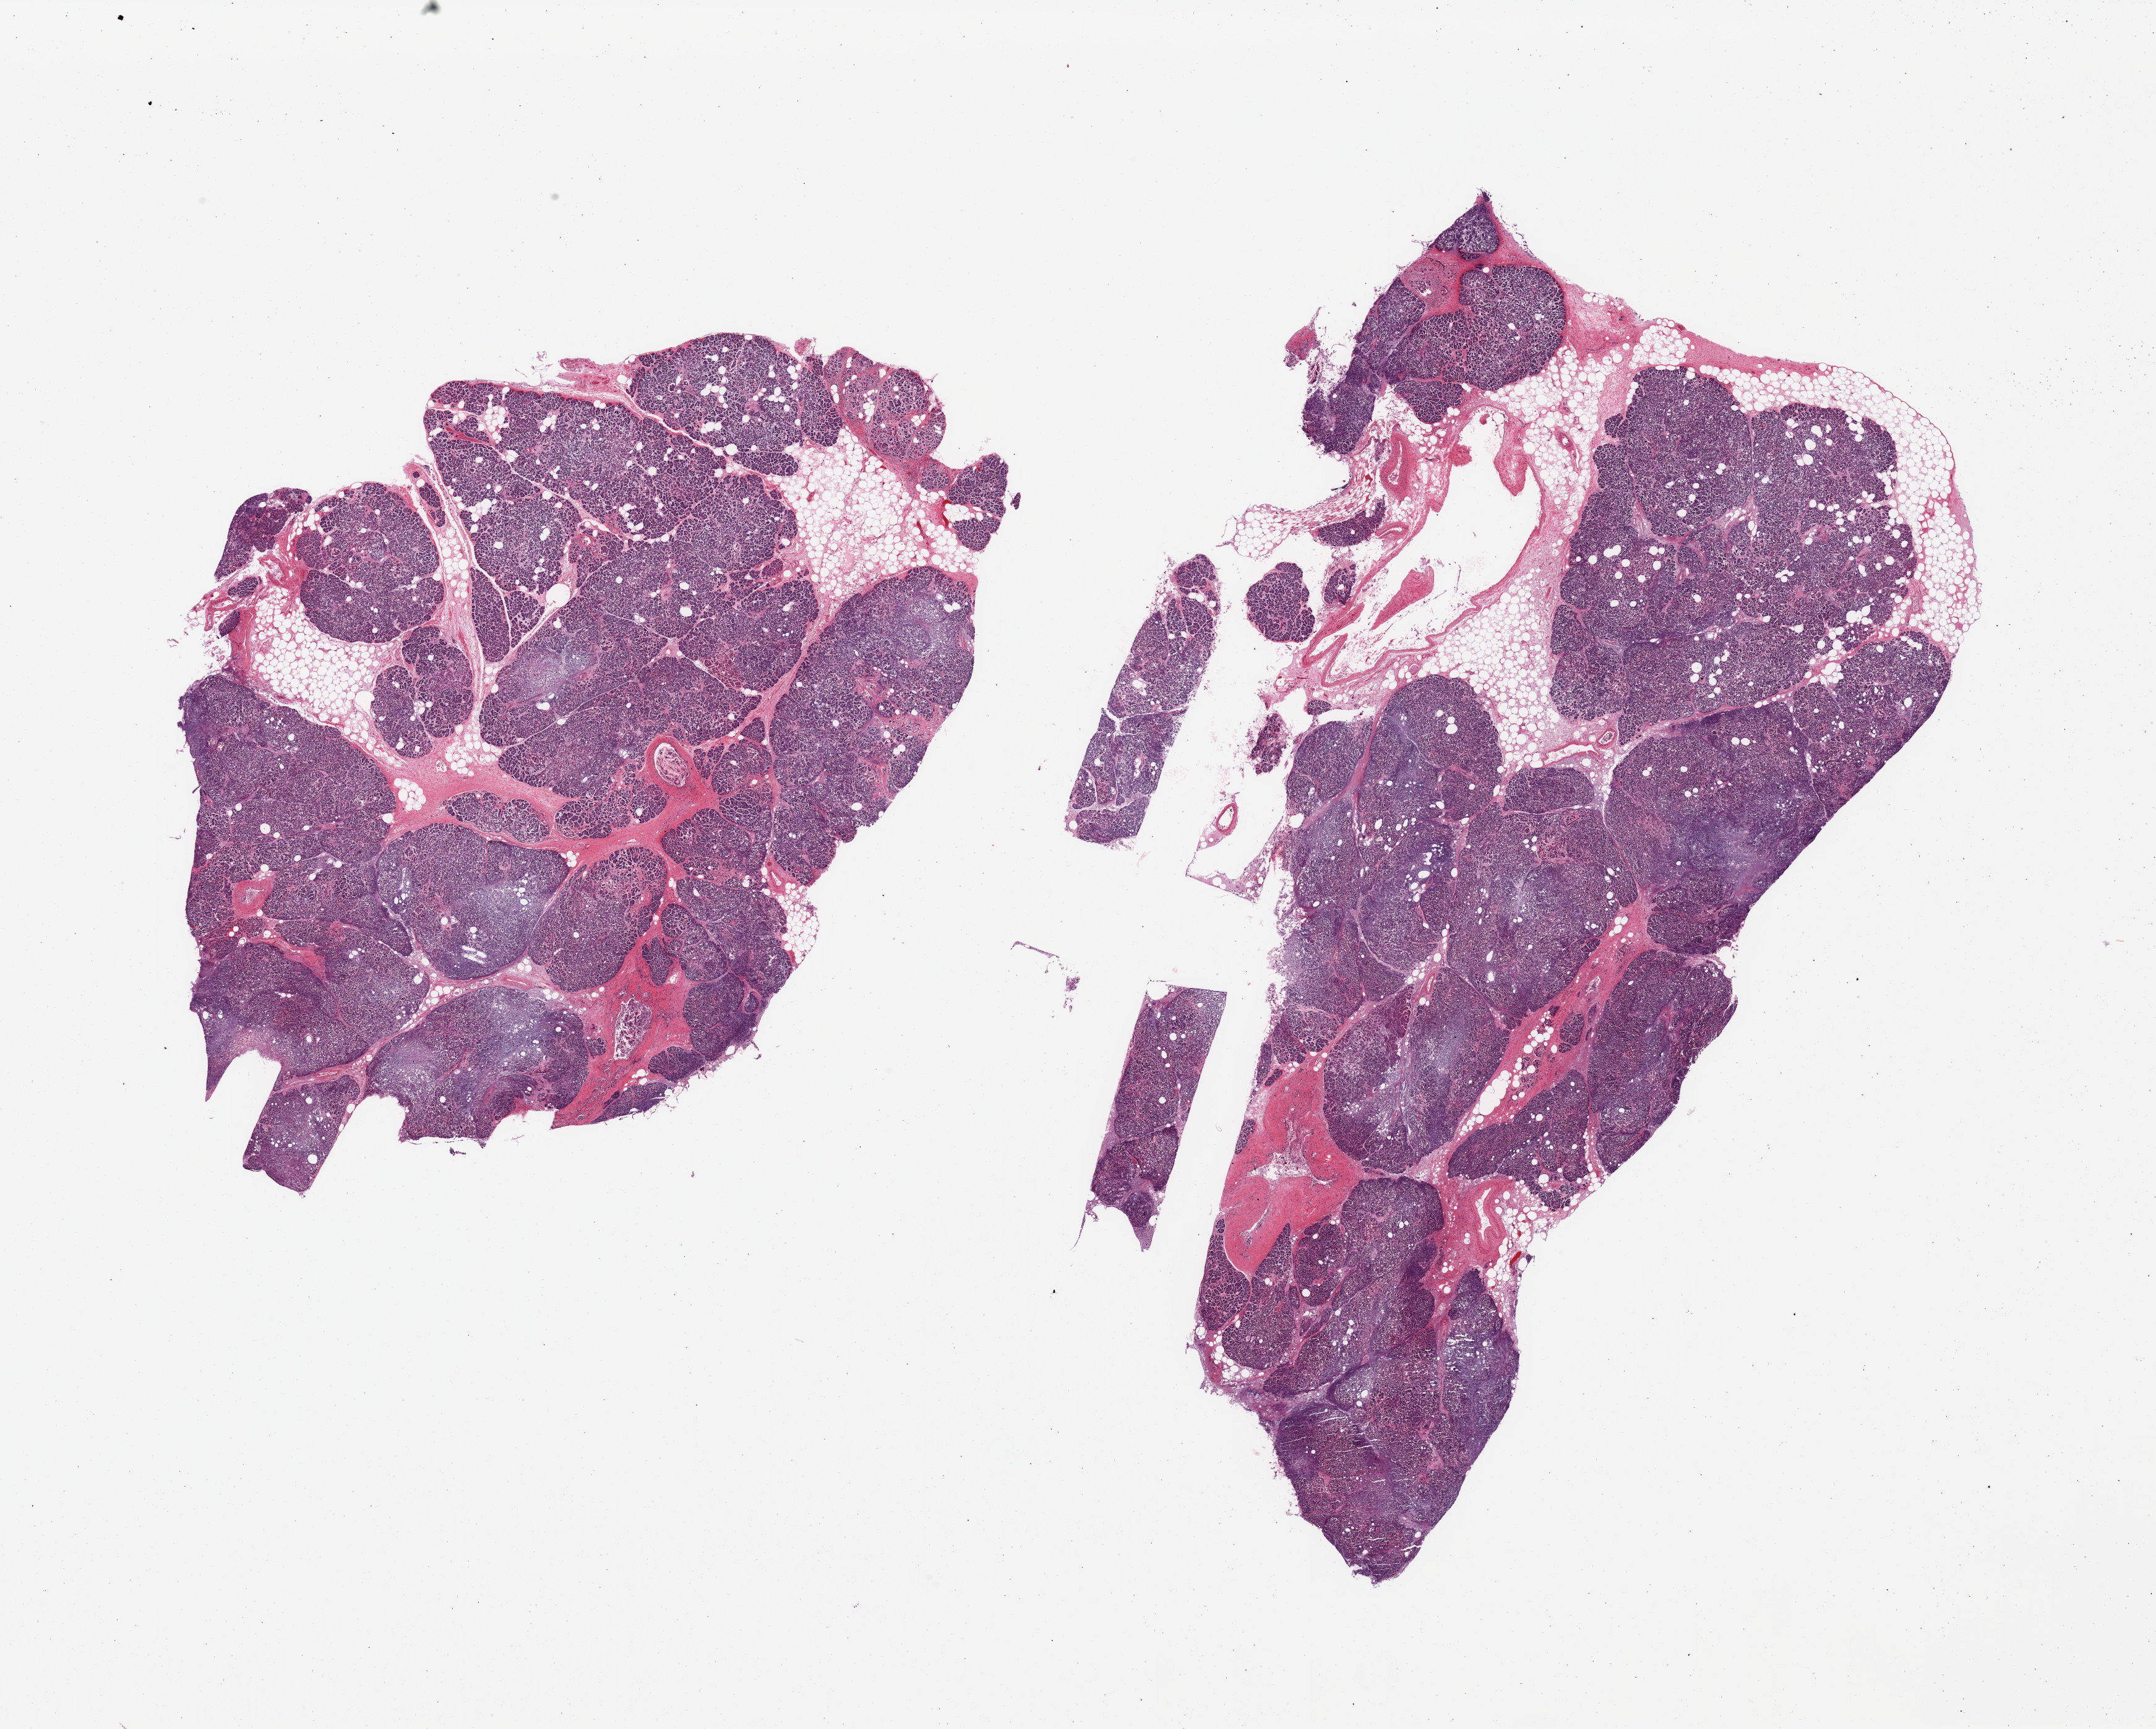
Haematoxylin and eosin whole-slide image, low-resolution overview of the scanned area, about 27.6 x 22.1 mm (slide scanned at 20x), PAXgene-fixed, paraffin-embedded tissue, section of pancreas (target tissue), donor tissue sample.
Review note (as recorded): 2 pieces; some areas are severely autolyzed.